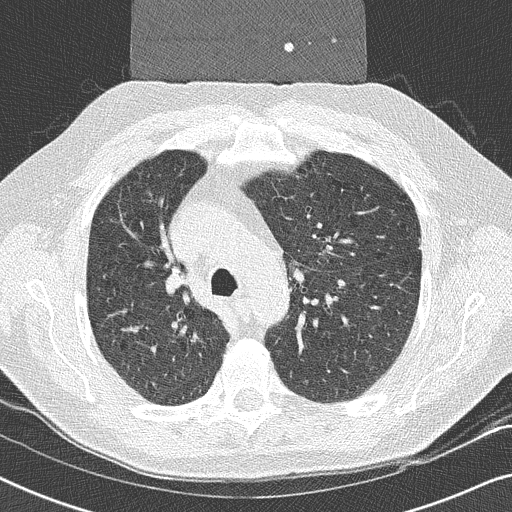
Low-dose screening chest CT, axial slice. Second screening round (one year after baseline). Lung window (W 1500 / L -600 HU). 2 mm slice thickness. Slice 83 of 252 in the series. 512 × 512 image matrix. Male, age 59 years at enrolment.
- Expert-annotated lung lesion, bounding box (x1, y1, x2, y2) in pixels: (138, 255, 201, 309).
- Reader record for this screening exam (exam-level; its link to the box is not recorded): non-calcified nodule or mass ≥4 mm, right upper lobe, 17 × 16 mm, smooth margins, soft tissue attenuation, pre-existing on the prior screen: yes.
- Official screen result: positive, other.
- Lung cancer was diagnosed 14 days after this screen: squamous cell carcinoma, NOS, right upper lobe, poorly differentiated (G3), stage IIA (AJCC 6th edition), 20 mm at pathology.